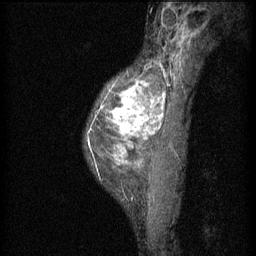
Breast MRI (dynamic contrast-enhanced), one sagittal slice. Slice 44 of 60 in the series (ordered by position). 3 images stored at this slice position (order not interpretable as contrast timing). 1.5 T. TE 4.2 ms, TR 11 ms. 256 × 256 image matrix, field of view 180 × 180 mm. Patient: female, 40 years.
Annotated regions visible in this slice (semi-automatic segmentation, software-assisted and operator-edited):
- analysis volume of interest (the breast-tissue region the enhancement analysis was run in; not a lesion): bounding box (x1, y1, x2, y2) in pixels: (87, 46, 171, 201)
- tumour enhancement mask (voxels above the 70 % enhancement threshold inside the analysis volume of interest): (89, 80, 166, 163)